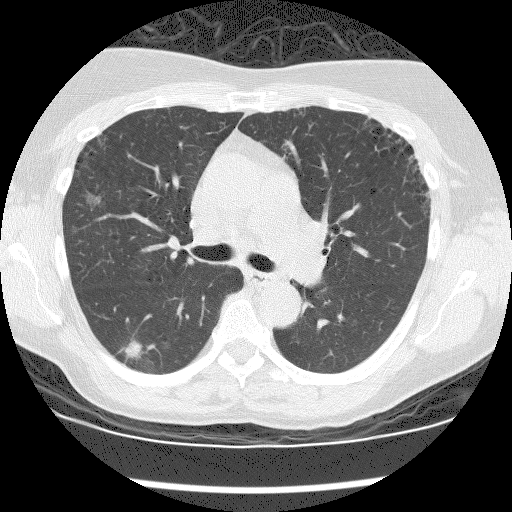
Low-dose screening chest CT, one axial slice. Reconstruction kernel BONE. 120 kVp. Lung window (W 1500 / L -600 HU). 2.5 mm slice thickness. 512 × 512 image matrix, field of view 320 × 320 mm.
Annotated regions visible in this slice (expert manual segmentation):
- lesion 1 (tumor, lower lobe of right lung): bounding box <124,340,156,359> (left, top, right, bottom; pixels)